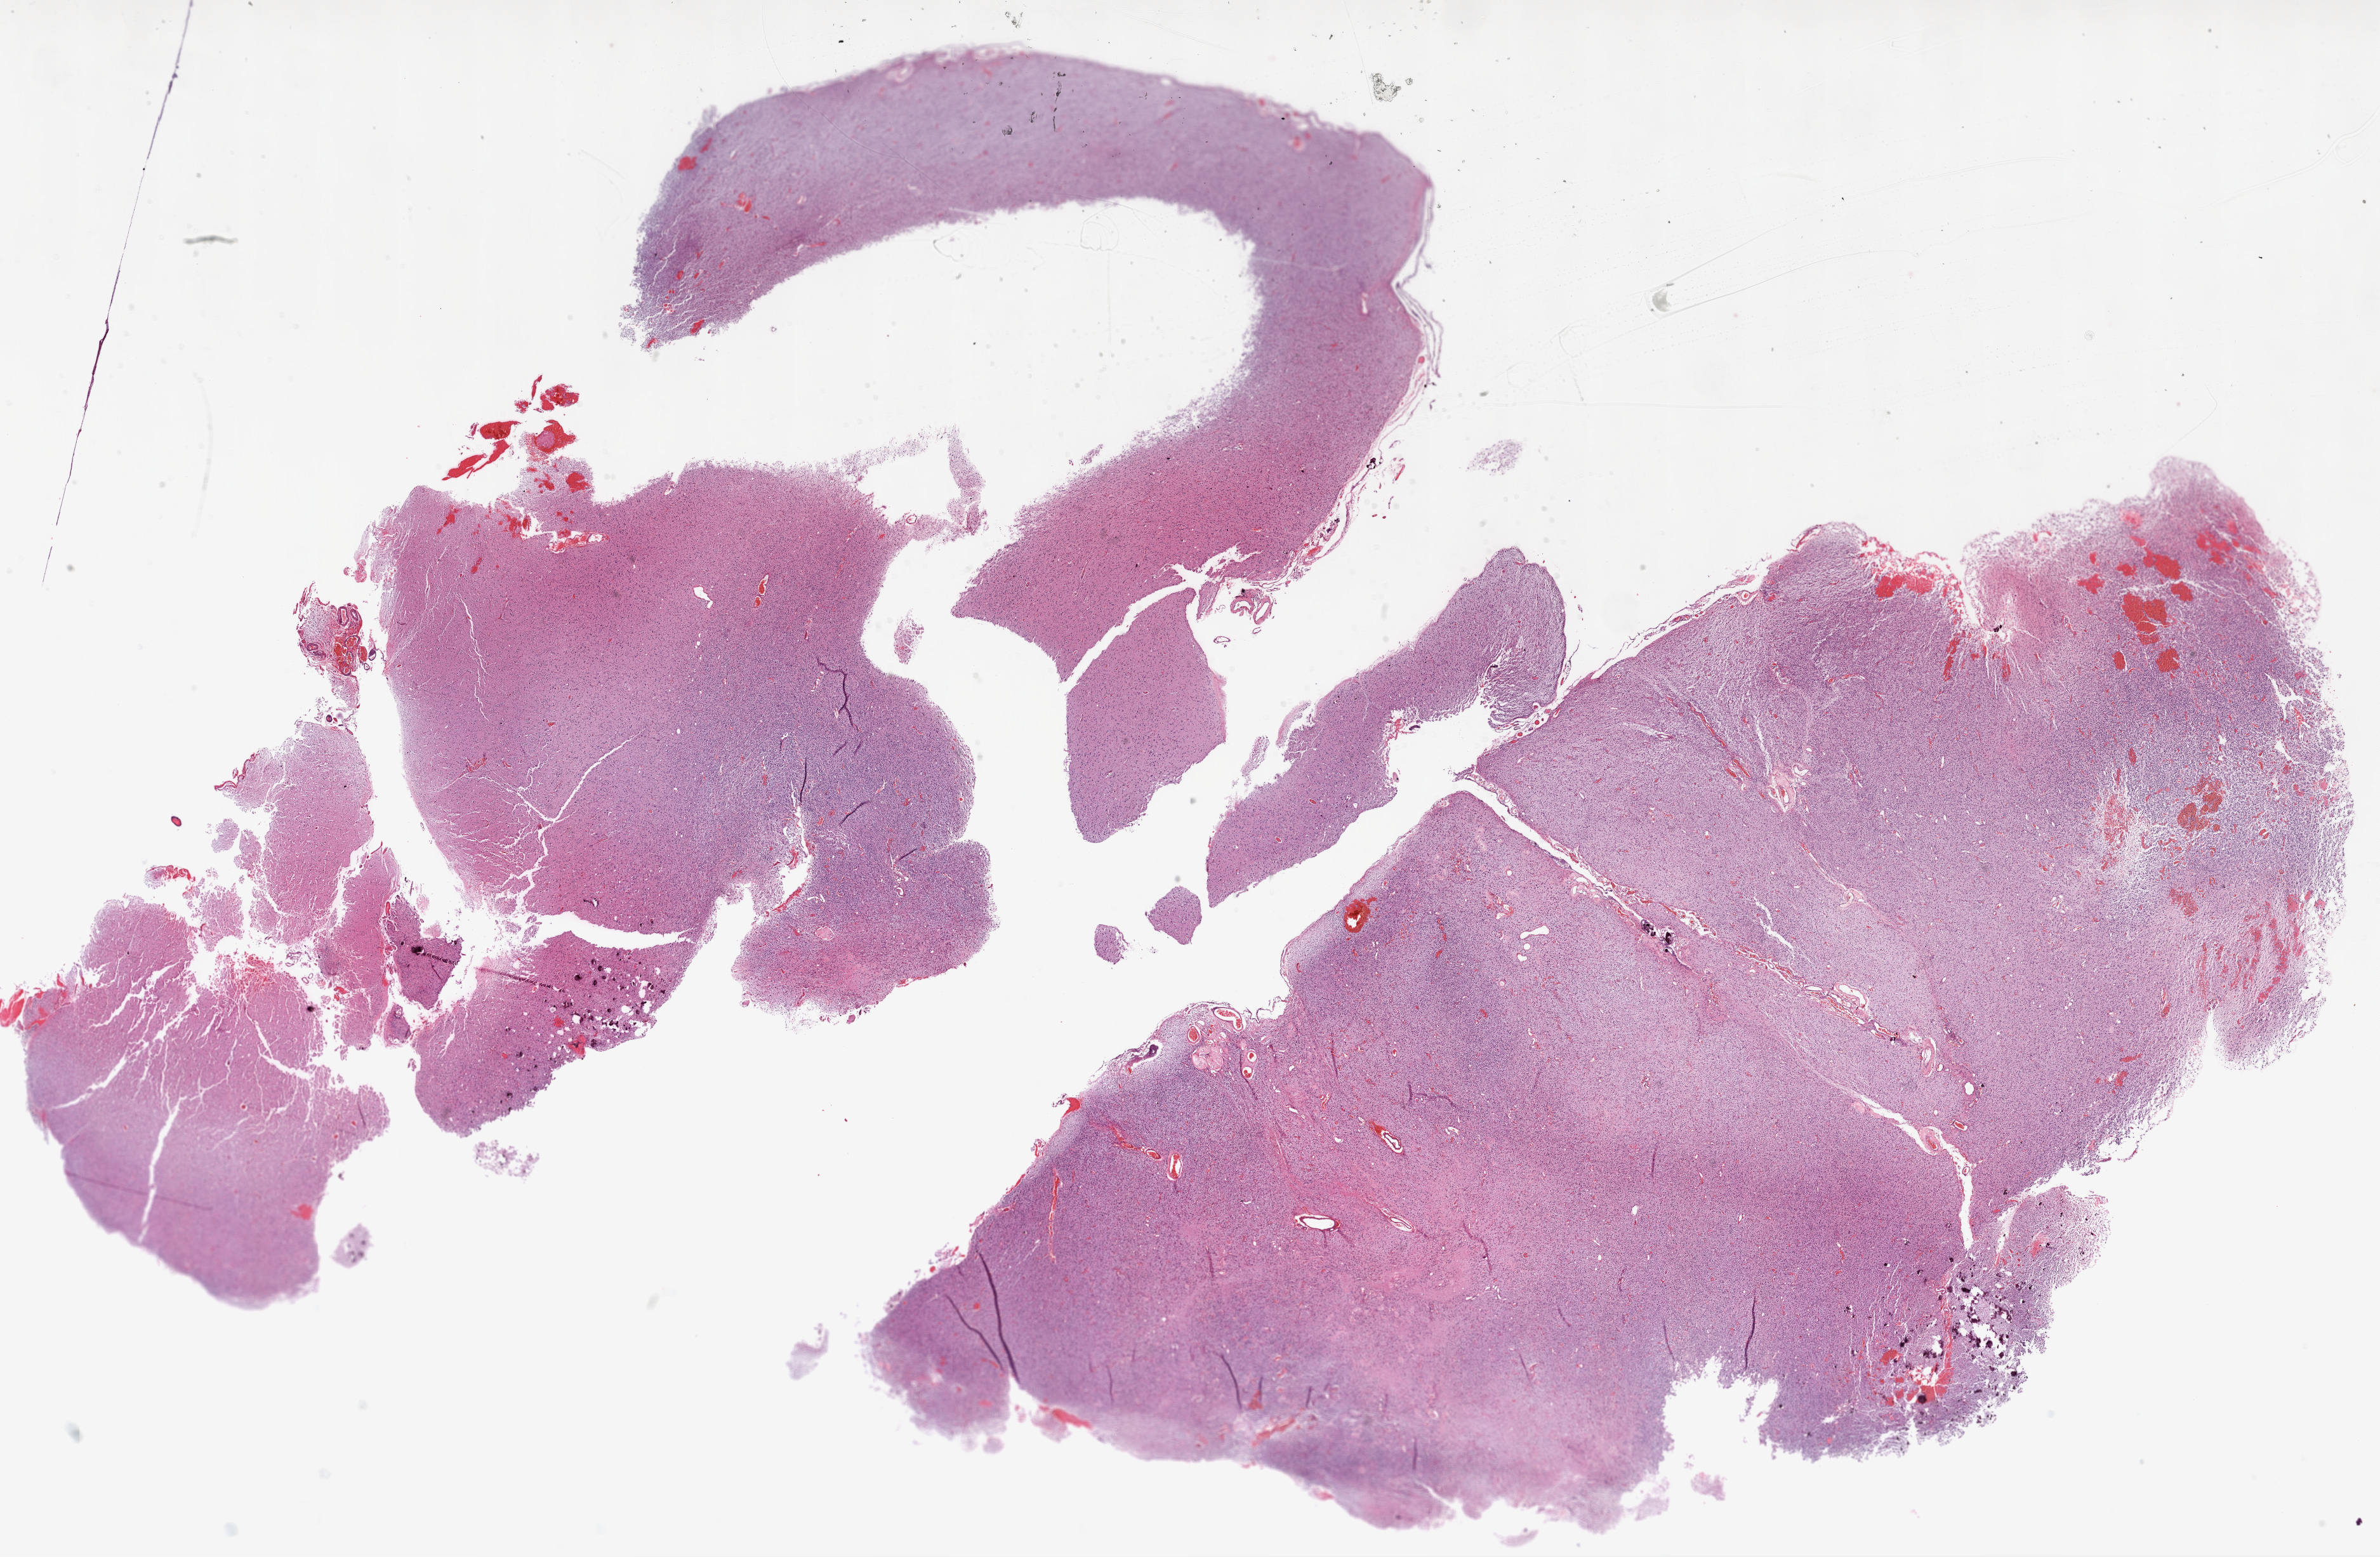
Whole-slide histology image, H&E-stained — a low-resolution overview of the entire scanned area, about 30.1 x 19.7 mm. FFPE section. Brain, primary tumour sample. Patient: male, age at initial diagnosis 54 years.
Diagnosis: Glioblastoma.